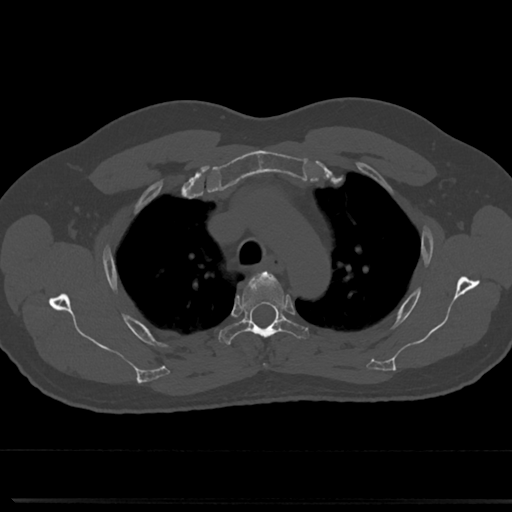
CT including the spine, one axial slice; position 556 of 817 along the scan axis; reconstruction kernel Br40s/3; 120 kVp; bone window (W 1800 / L 400 HU); 512 × 512 image matrix, field of view 355 × 355 mm. Male patient, age 61 years. Case-level facts recorded for this patient, not image findings: primary cancer: prostate.
Outlined on this slice (semi-automatic segmentation, software-assisted and operator-edited):
- T3 vertebra: box from (x=264, y=363) to (x=268, y=367) px
- T4 vertebra: (x=219, y=271)–(x=310, y=344)